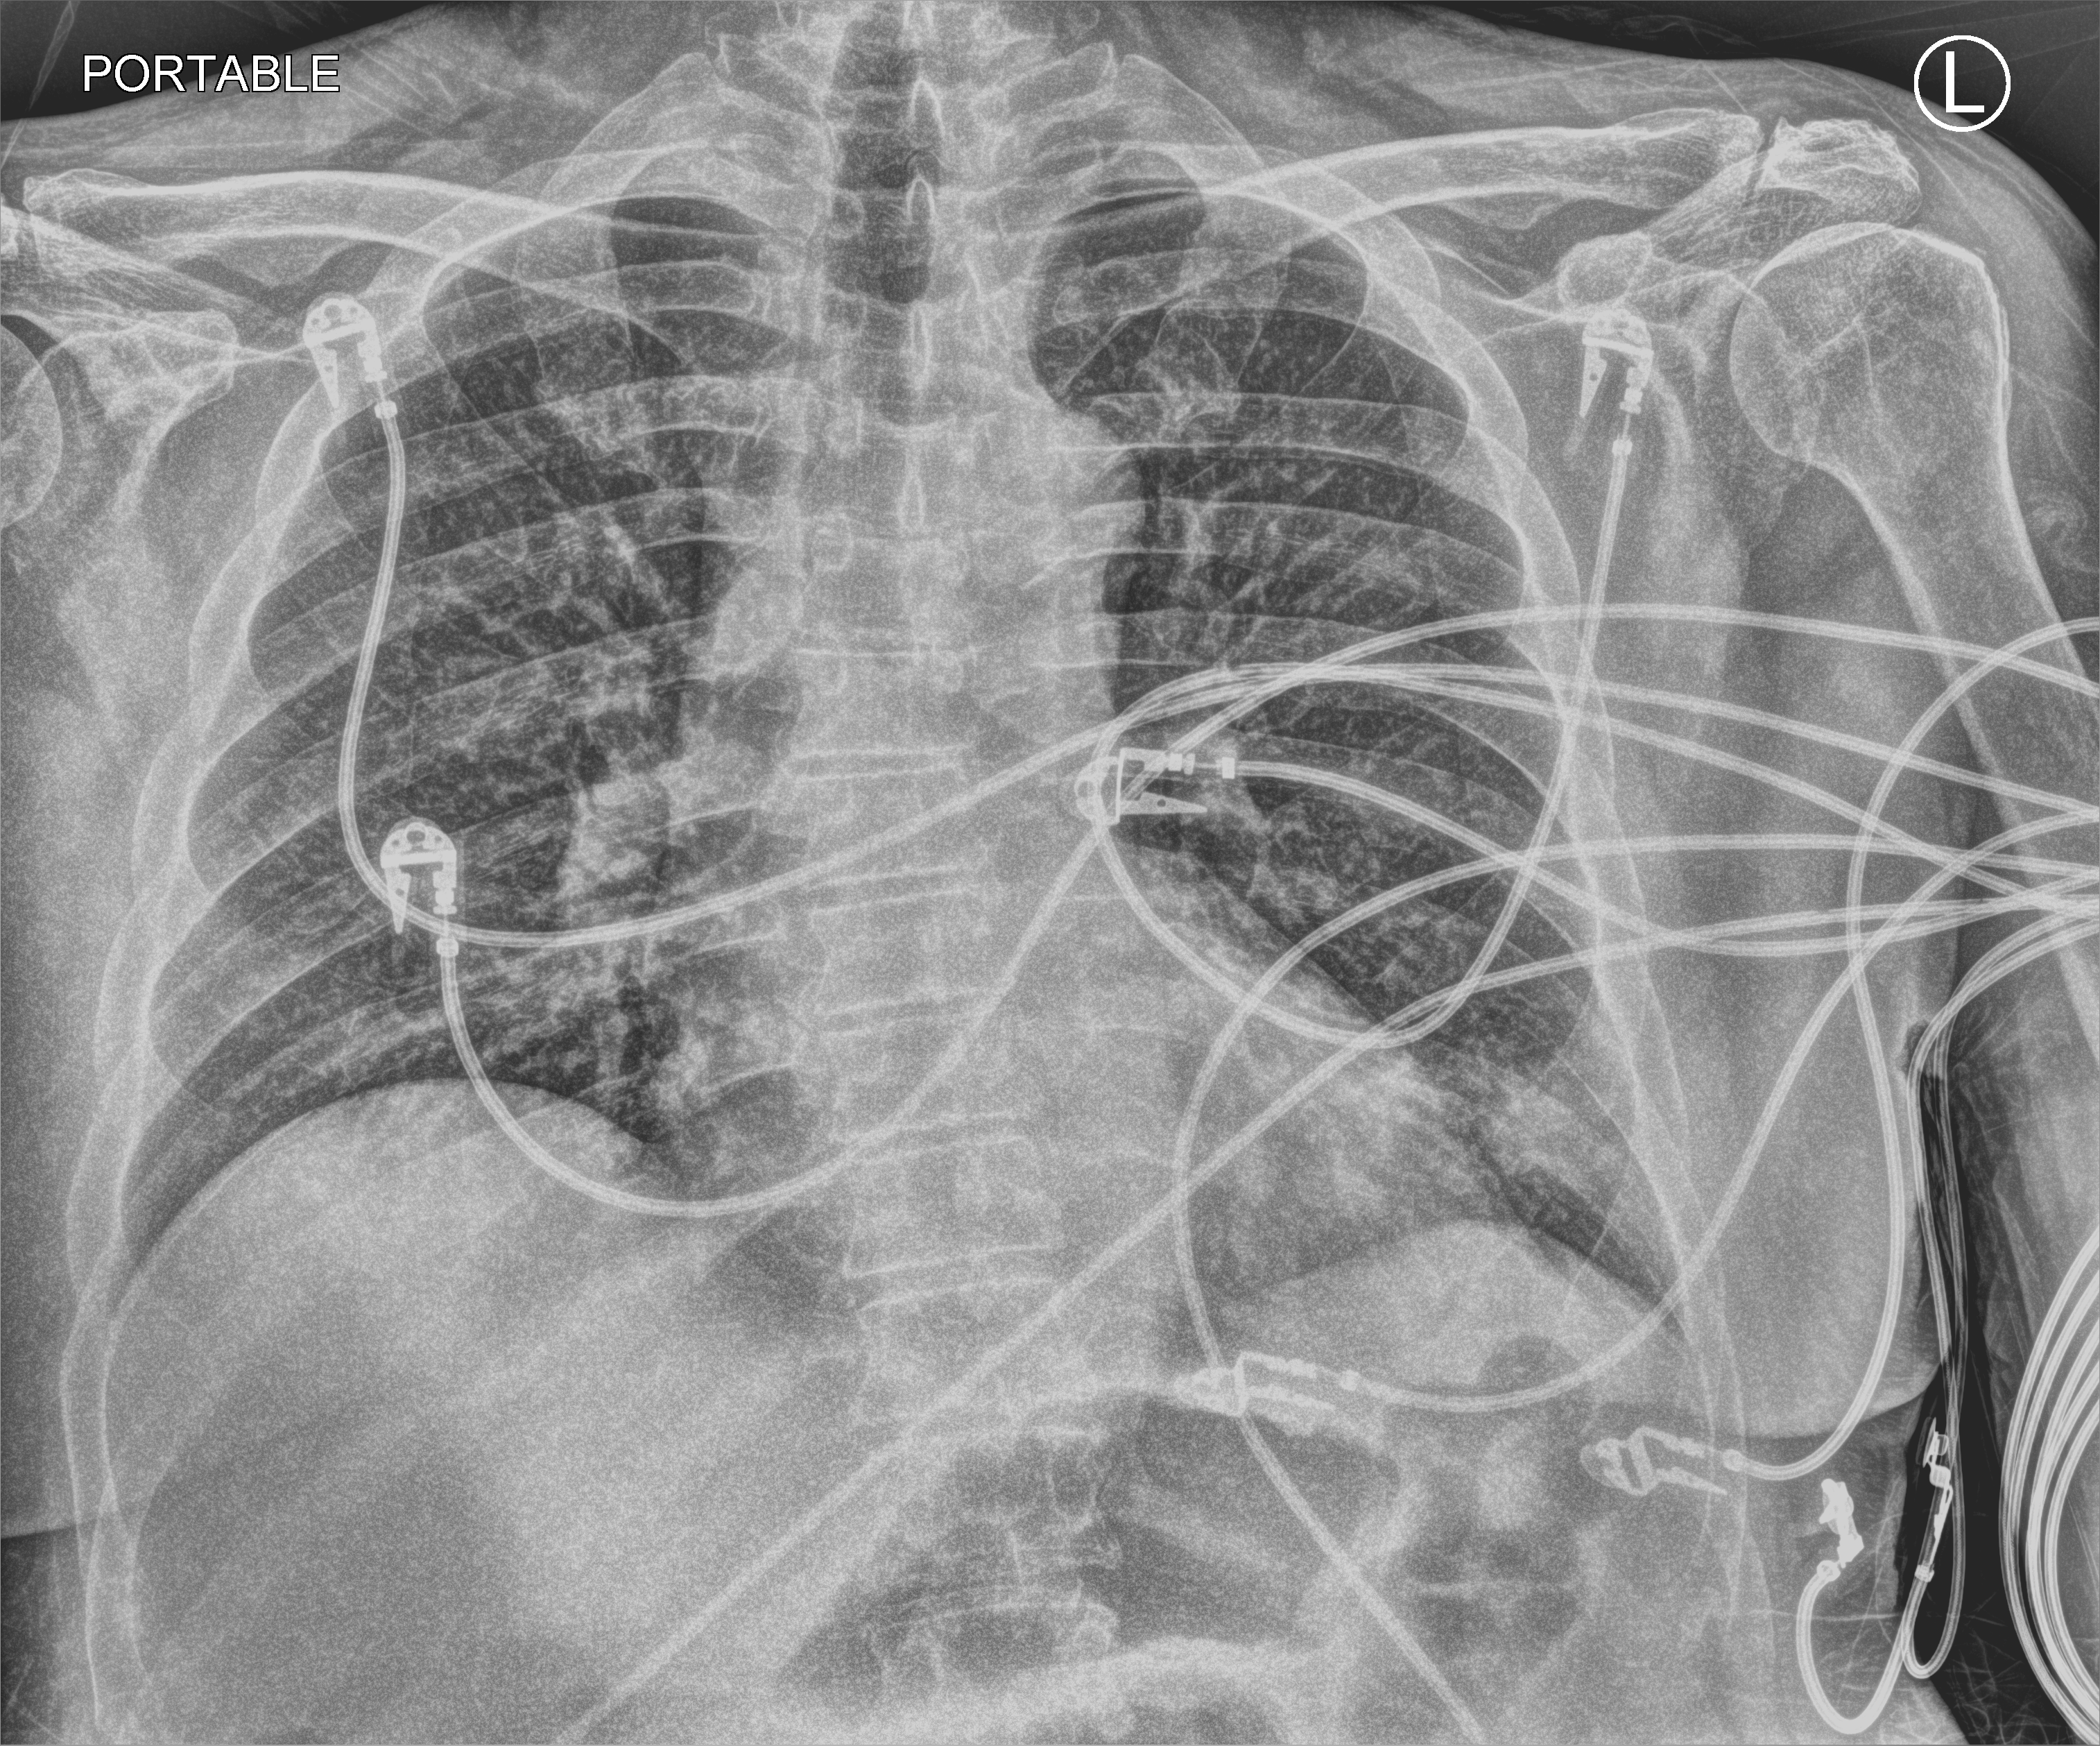
Portable chest radiograph; anteroposterior (AP) projection. Male patient hospitalised with COVID-19, age 60–74 years.
Hospital-stay facts (about this admission, not read from this image; timing relative to this image not recorded):
- admitted to intensive care during this hospital stay: yes
- length of hospital stay: 16 days
- mechanically ventilated during this hospital stay: yes